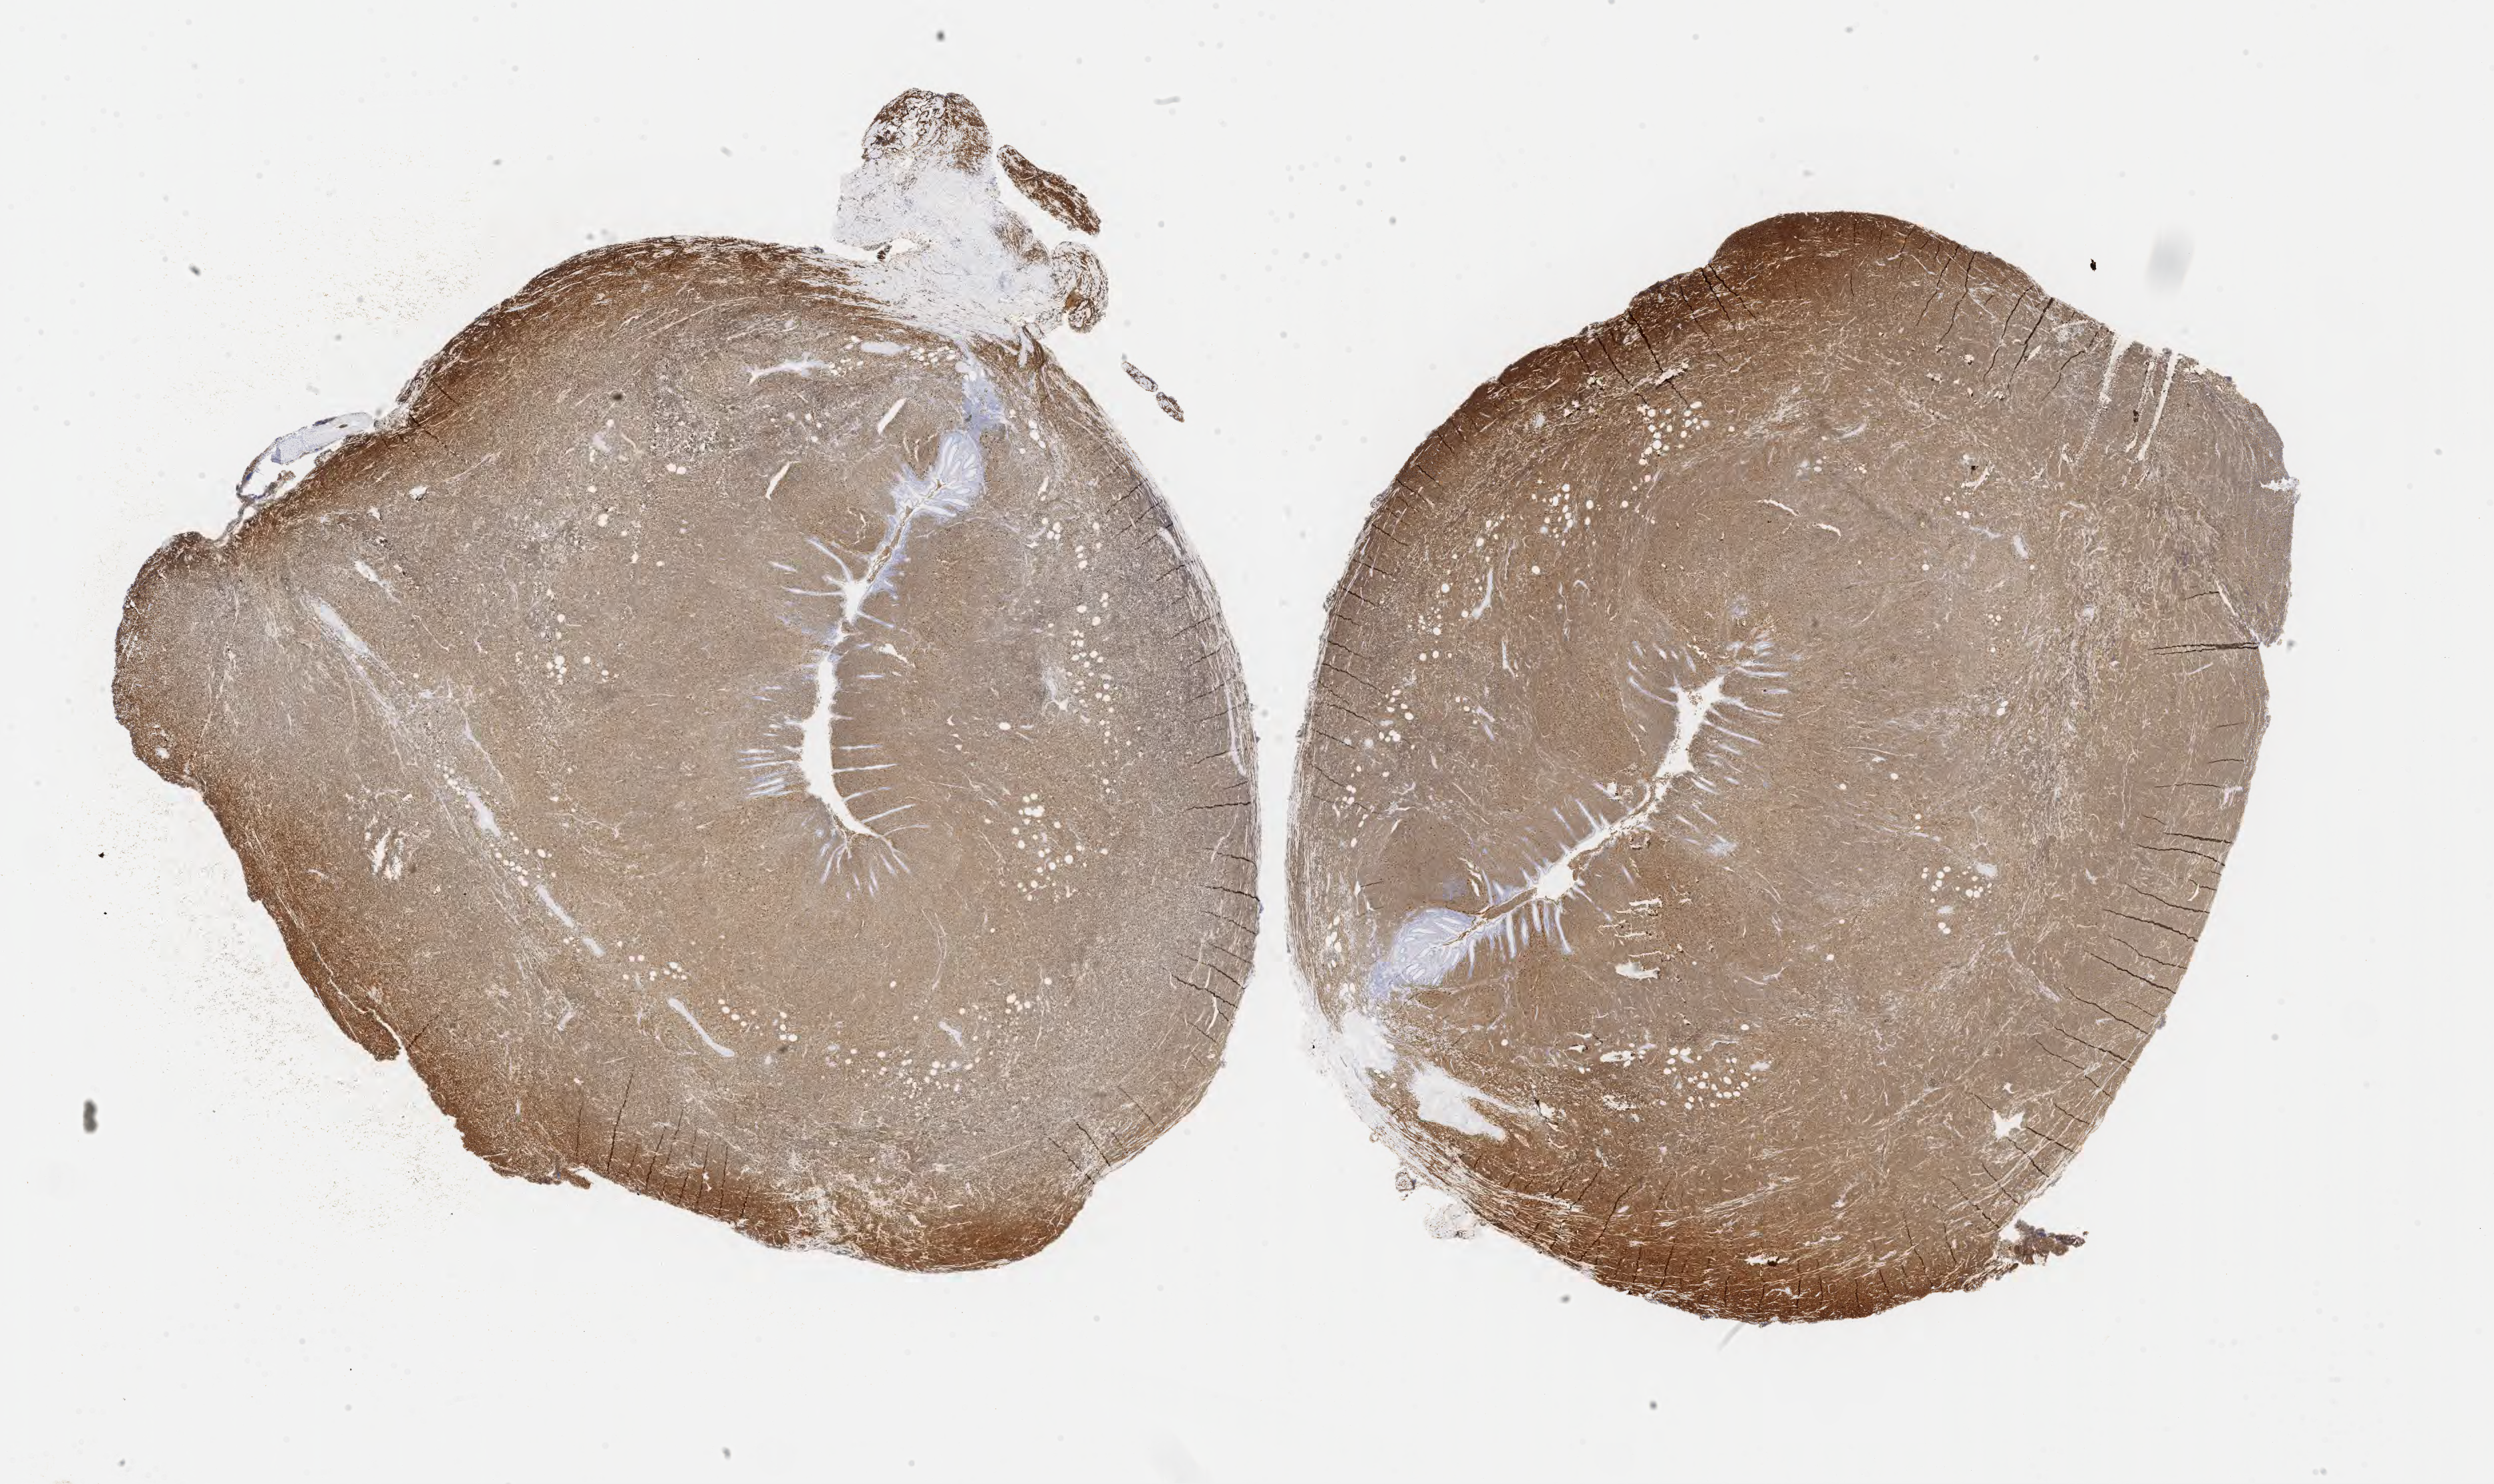
Immunohistochemistry (IHC) whole-slide image stained for CD10 — whole scanned area (about 30.2 x 18.0 mm) shown as a low-resolution overview. Tumor tissue. Patient male; 63 years old.
Histologic diagnosis: Diffuse large B-cell lymphoma, NOS.